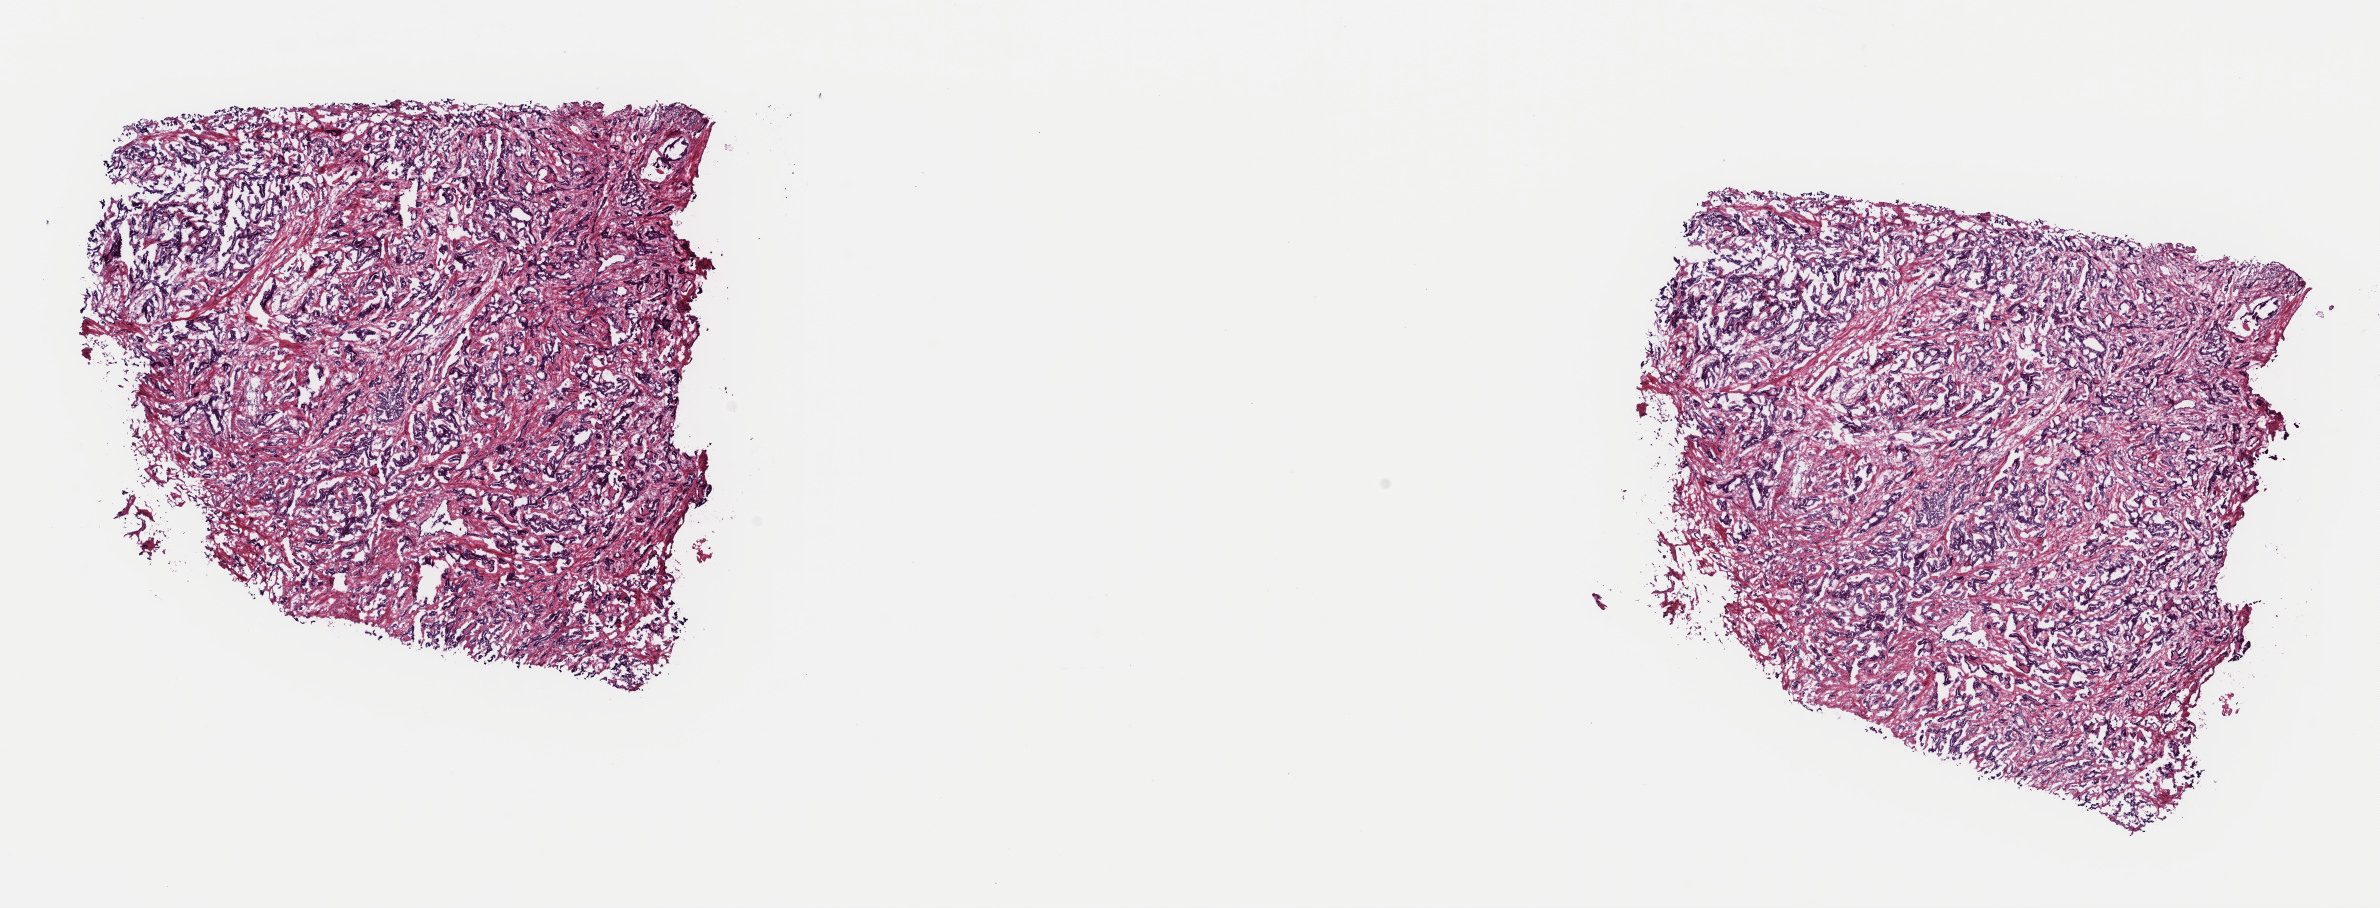
H&E whole-slide image, shown as a low-resolution overview of the whole scanned area (about 18.8 x 7.2 mm, acquisition: 40x scan); frozen section; sample: primary tumour, prostate. Patient: male, age at initial diagnosis 63 years. Gleason score: 7 (3+4). Slide review estimates, as recorded: tumour cells 60%, tumour nuclei 80%, normal cells 0%, stromal cells 40%, necrosis 0%. Inflammatory infiltration, as recorded: lymphocyte infiltration 0%, monocyte infiltration 0%, neutrophil infiltration 0%.
Laterality: bilateral. Pathologic diagnosis: Acinar cell carcinoma (prostate gland). Lymph nodes positive (case pathology): 0 of 9 examined.